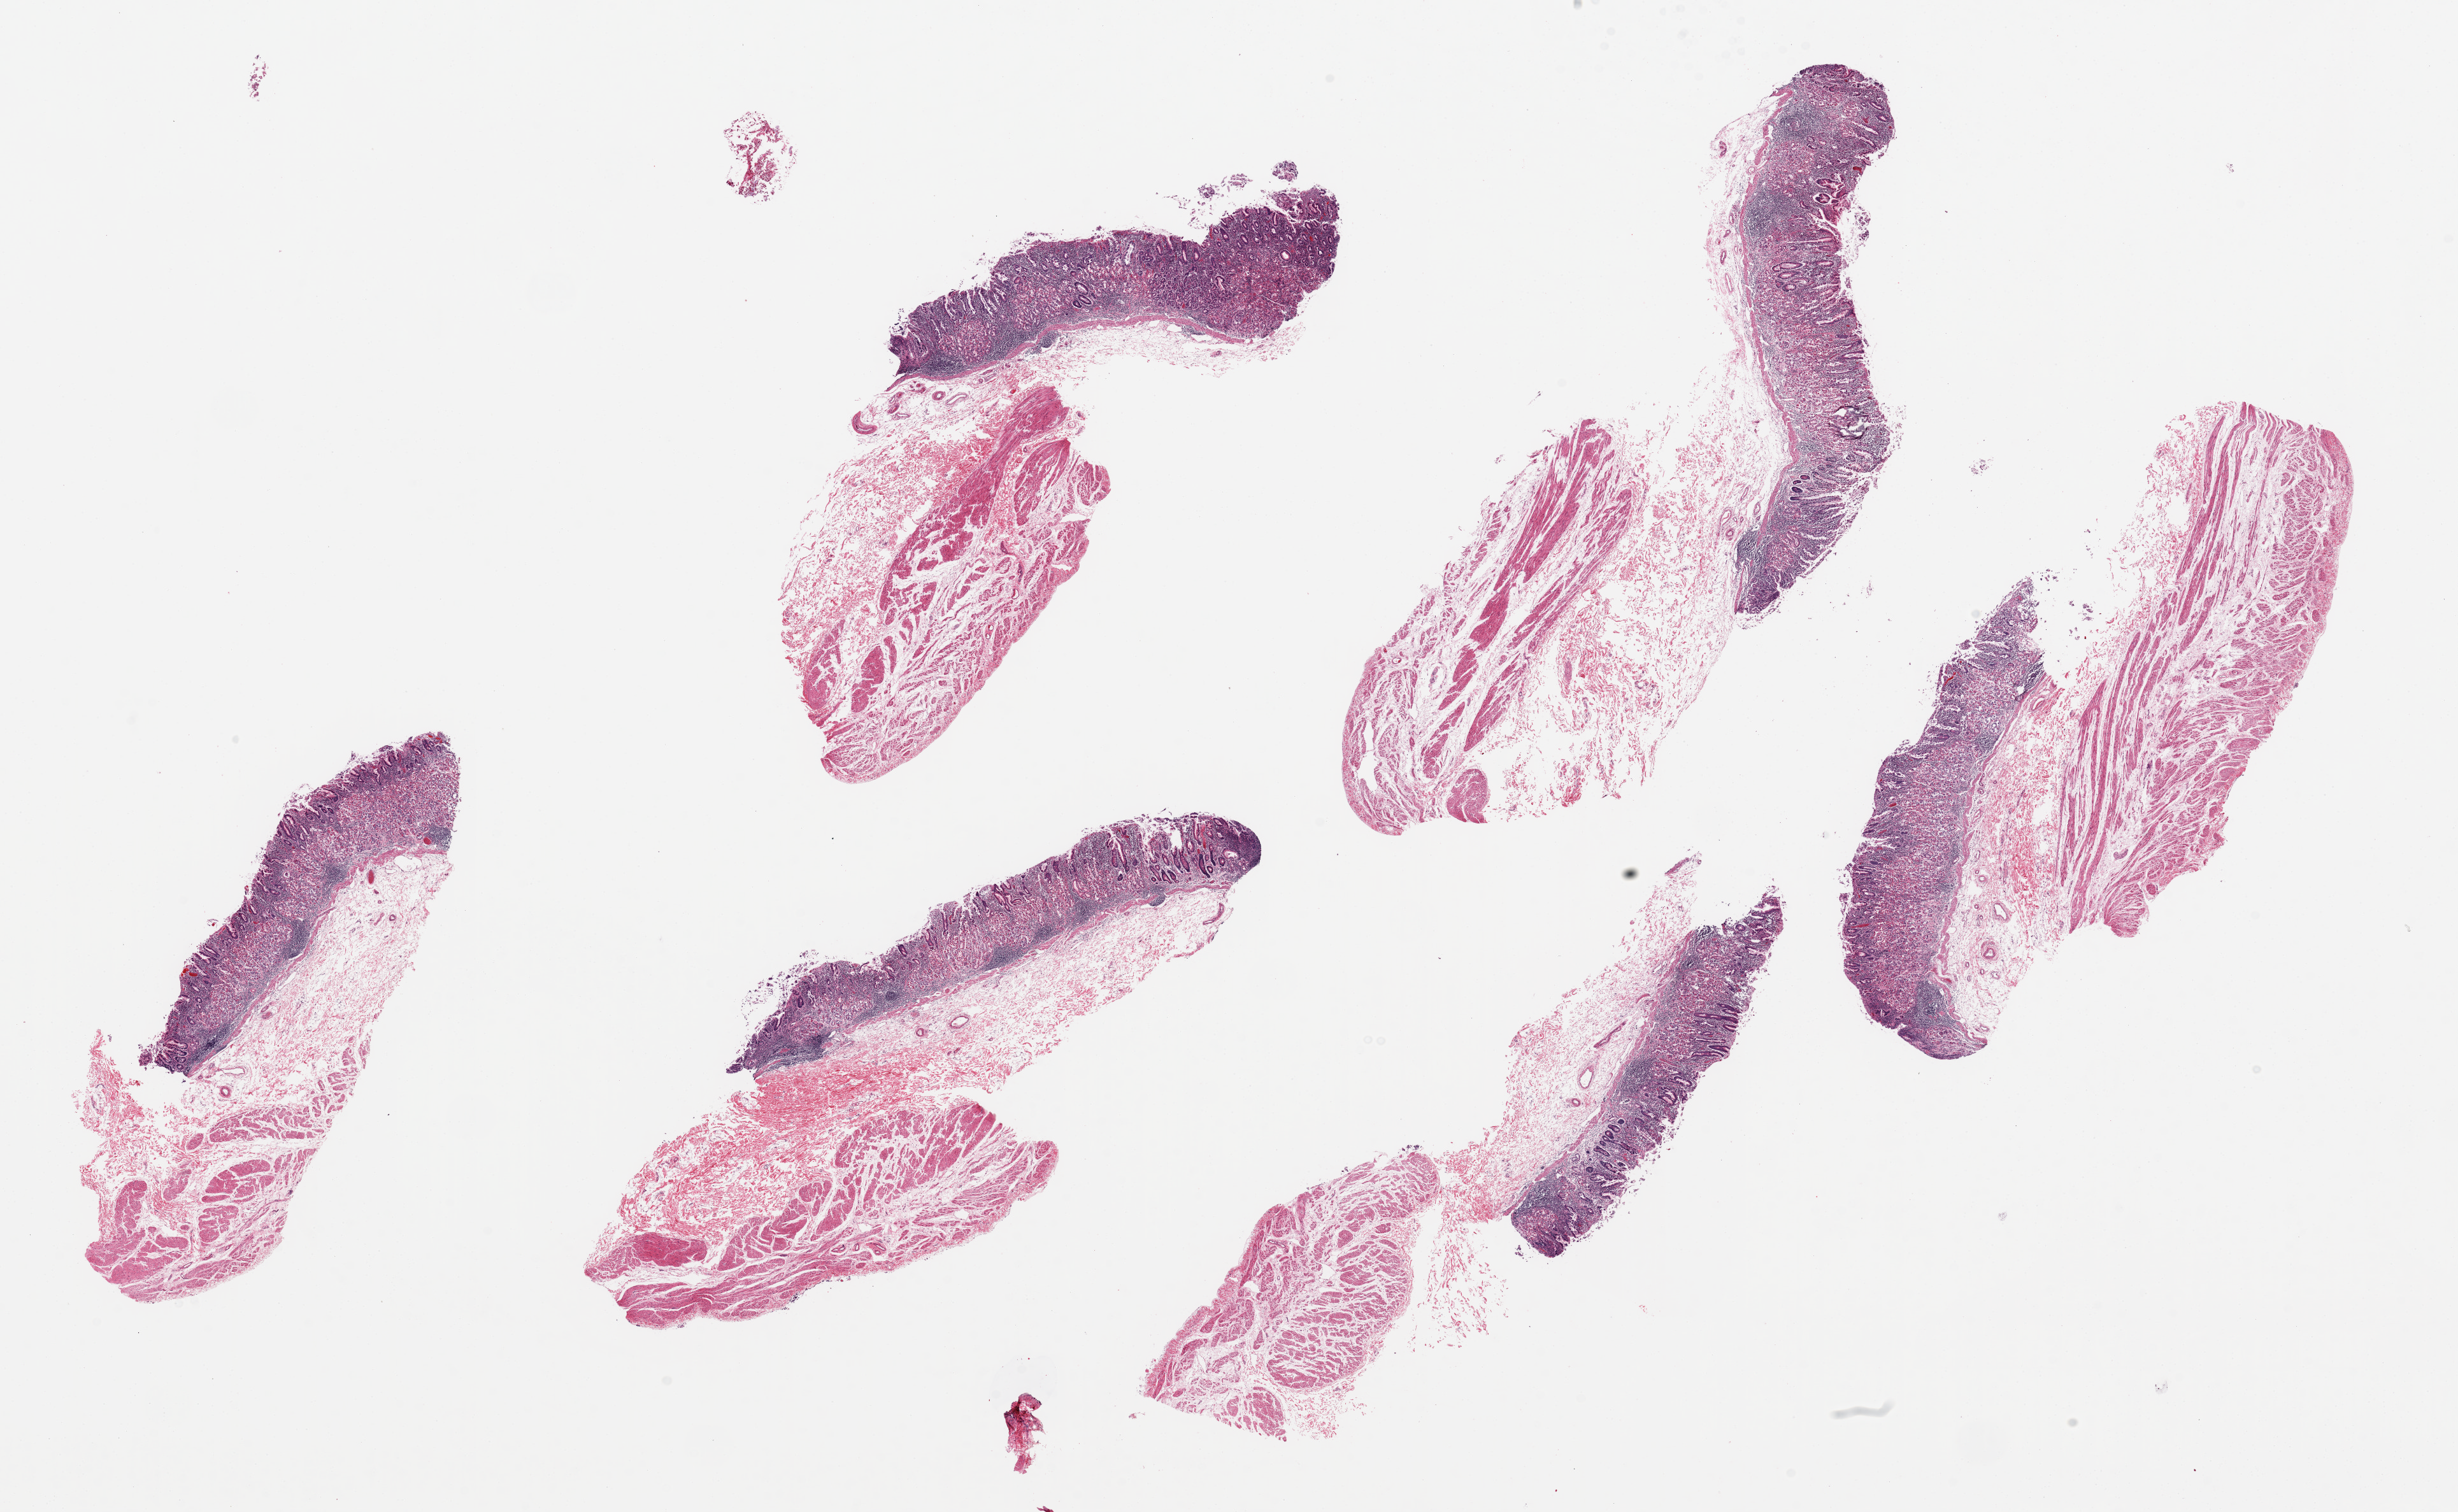
Hematoxylin and eosin (H&E) whole-slide image, brightfield — low-resolution overview of the scanned area, about 30.5 x 18.8 mm (acquisition: 20x scan), PAXgene-fixed, paraffin-embedded tissue, target tissue: stomach, donor tissue sample. Donor sex: male.
Review note (as recorded): 6 pieces up to 11x3.8 mm; largely autolyzed mucosa, patchy preservation; muscle edematous; extensive chronic gastritis.